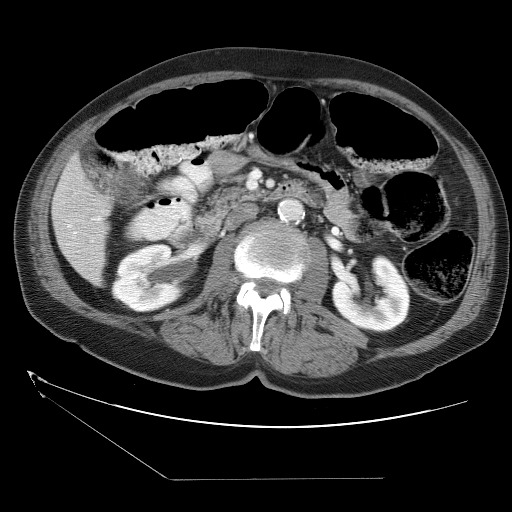
Contrast-enhanced abdominal CT (liver protocol), one axial slice; reconstruction kernel STANDARD; 120 kVp; soft-tissue window (W 400 / L 40 HU); 5 mm slice thickness; 512 × 512 image matrix, field of view 400 × 400 mm. Case-level facts recorded for this patient, not image findings: diagnosis: hepatocellular carcinoma (patient treated with transarterial chemoembolisation; whether this scan precedes or follows treatment is not stated here); TNM stage (as recorded): Stage-II; Child-Pugh class: A; tumour differentiation: moderately differentiated; tumour nodularity: multinodular.
Annotated regions visible in this slice (semi-automatic segmentation, software-assisted and operator-edited):
- liver parenchyma outside the tumour (the mass and vessels are separate outlines, so this box may not span the whole liver): bounding box [x1, y1, x2, y2] px = [52, 152, 112, 284]
- liver vessels: [67, 224, 93, 243]